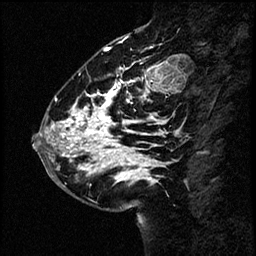
Breast MRI (dynamic contrast-enhanced), one sagittal slice. Dynamic contrast-enhanced study with each time point stored as its own series, time point 2 of 4 at this slice position (early post-contrast, ordered by acquisition time). 1.5 T. TE 4.2 ms, TR 17.6 ms. 2 mm slice thickness. 256 × 256 image matrix, field of view 200 × 200 mm. Patient: female, 43 years. Case-level facts recorded for this patient, not image findings: setting: breast cancer imaged before/during neoadjuvant chemotherapy.
Outlined on this slice (semi-automatic segmentation, software-assisted and operator-edited):
- analysis volume of interest (the breast-tissue region the enhancement analysis was run in; not a lesion): box from (x=37, y=58) to (x=169, y=191) px
- tumour enhancement mask (voxels above the 100 % enhancement threshold inside the analysis volume of interest): (x=38, y=65)–(x=163, y=181)